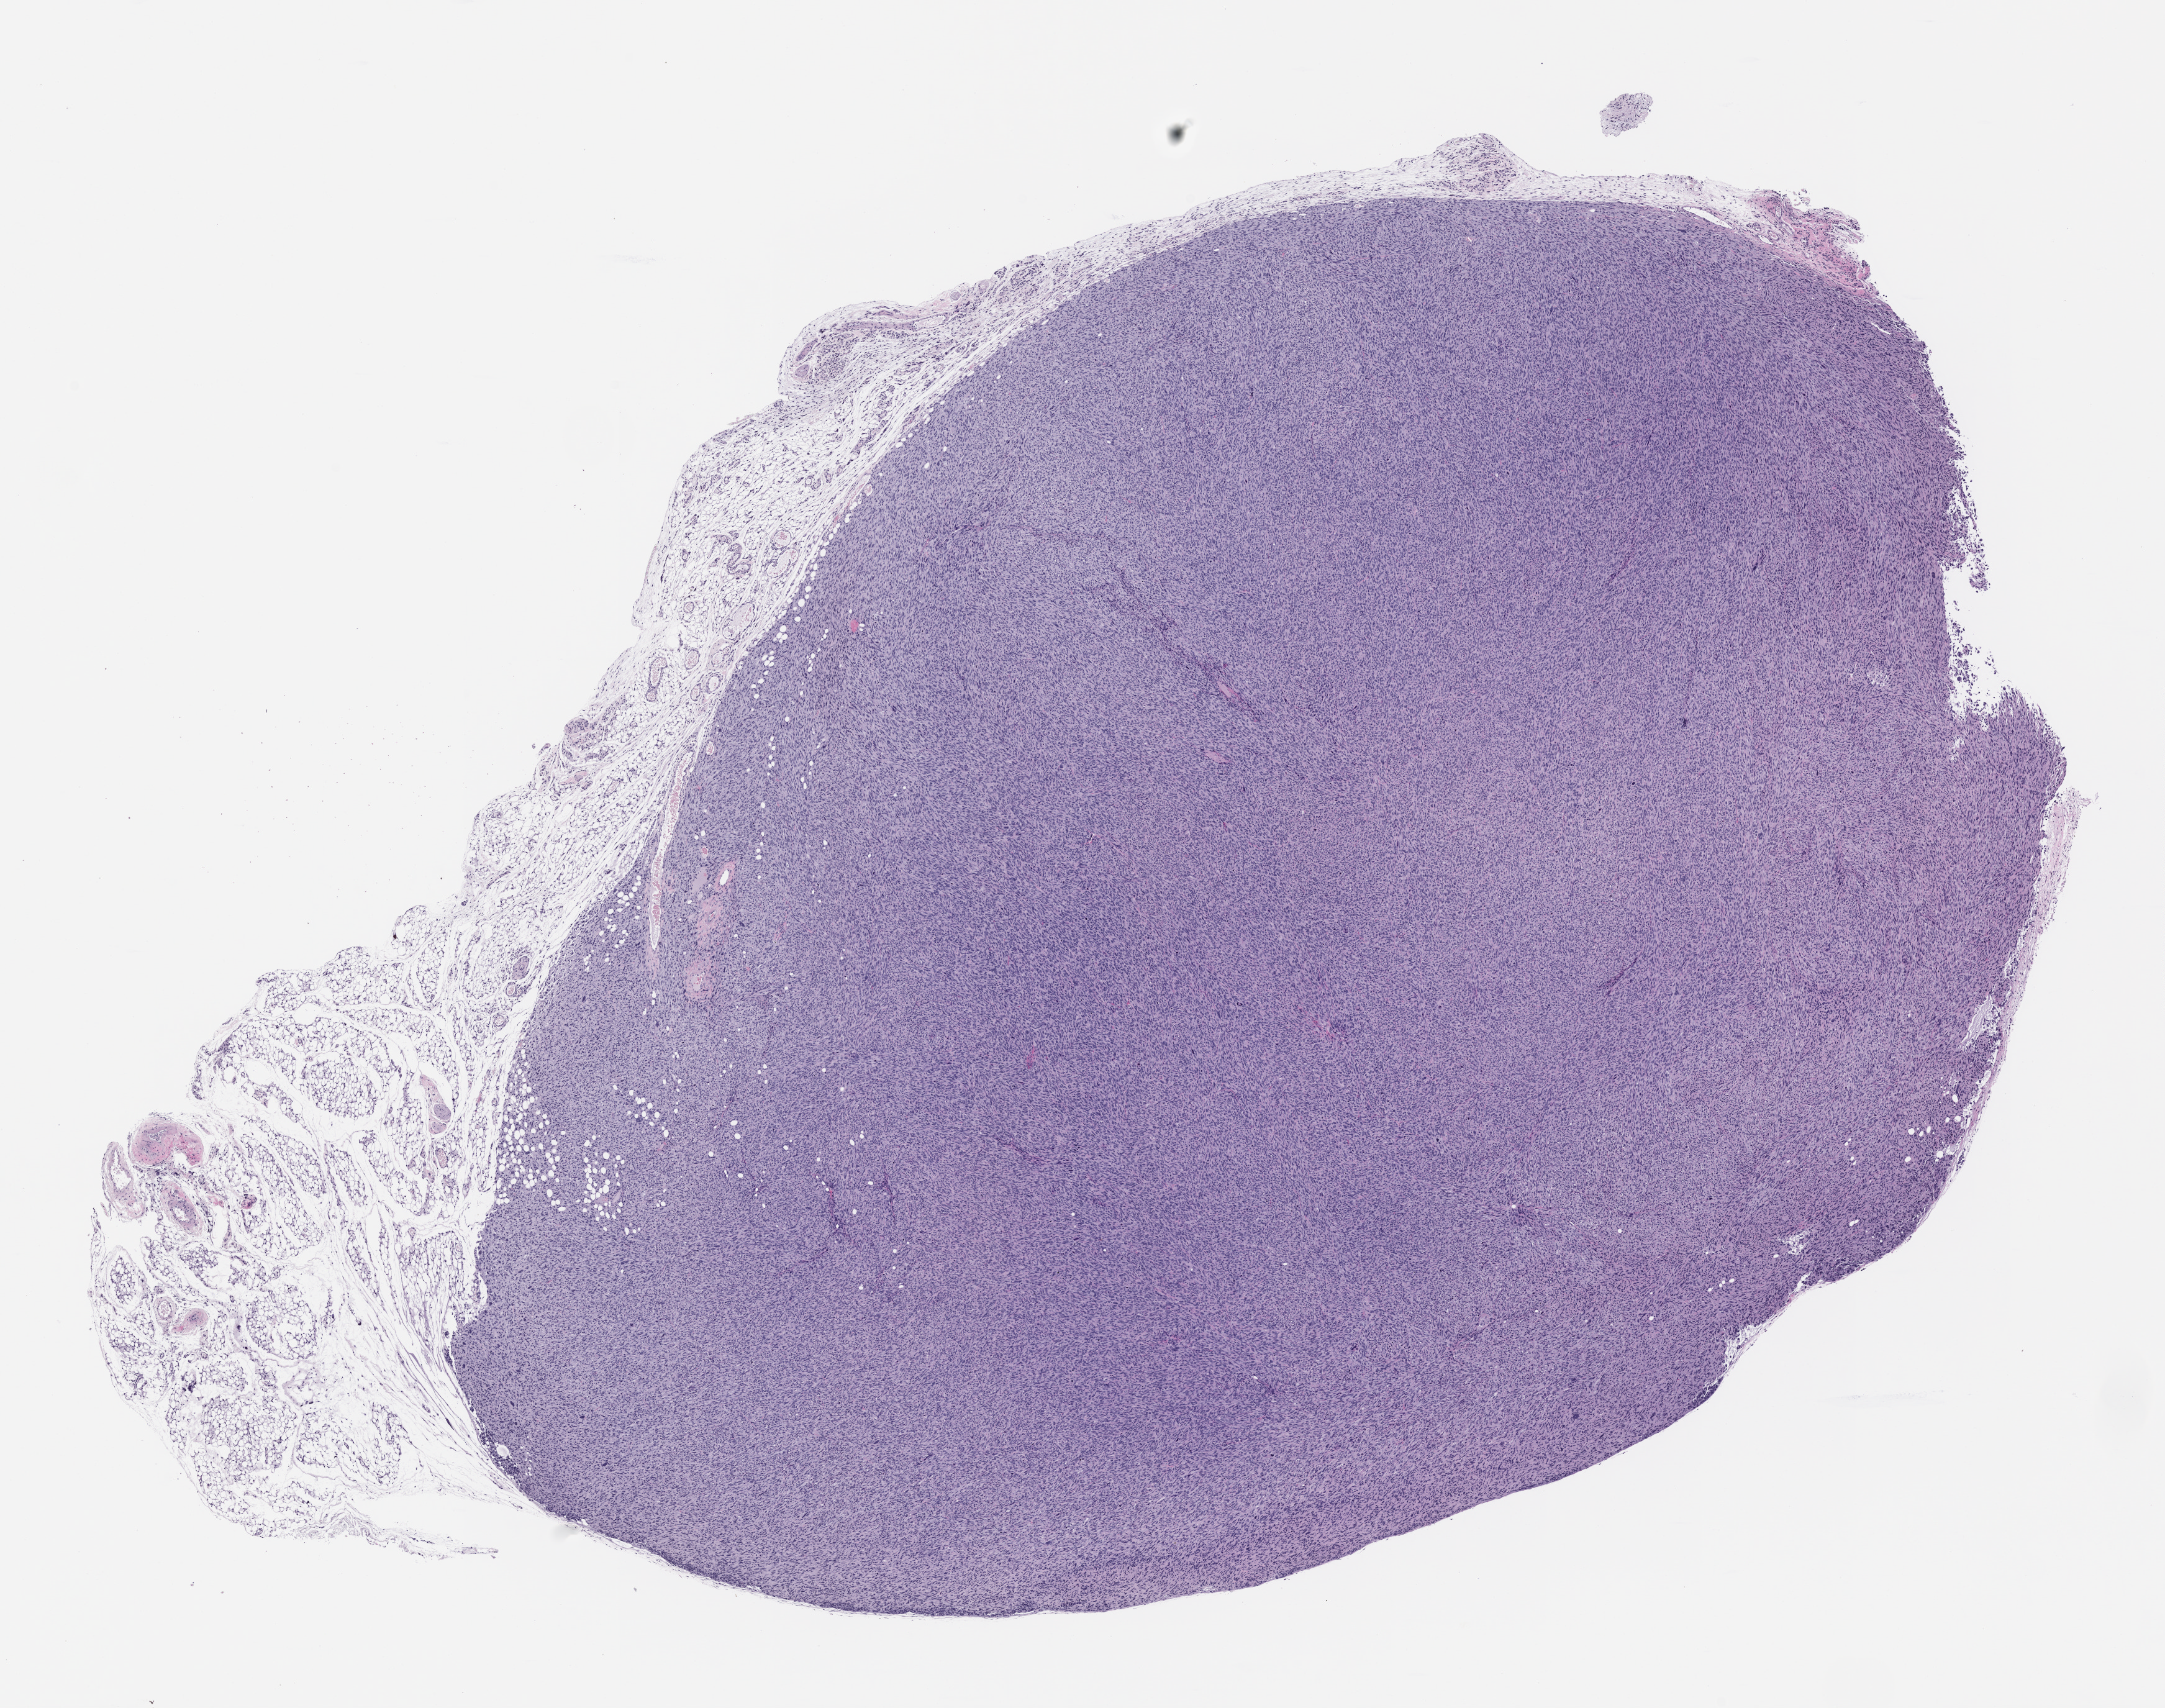
Hematoxylin and eosin (H&E) whole-slide image of a patient-derived xenograft (PDX) tumor grown in a mouse, passage 1 — shown as a low-resolution overview of the whole scanned area (about 14.0 x 11.1 mm); formalin-fixed, paraffin-embedded (FFPE) tissue; tumor site category: musculoskeletal.
• originating patient diagnosis: Non-Rhabdo. soft tissue sarcoma